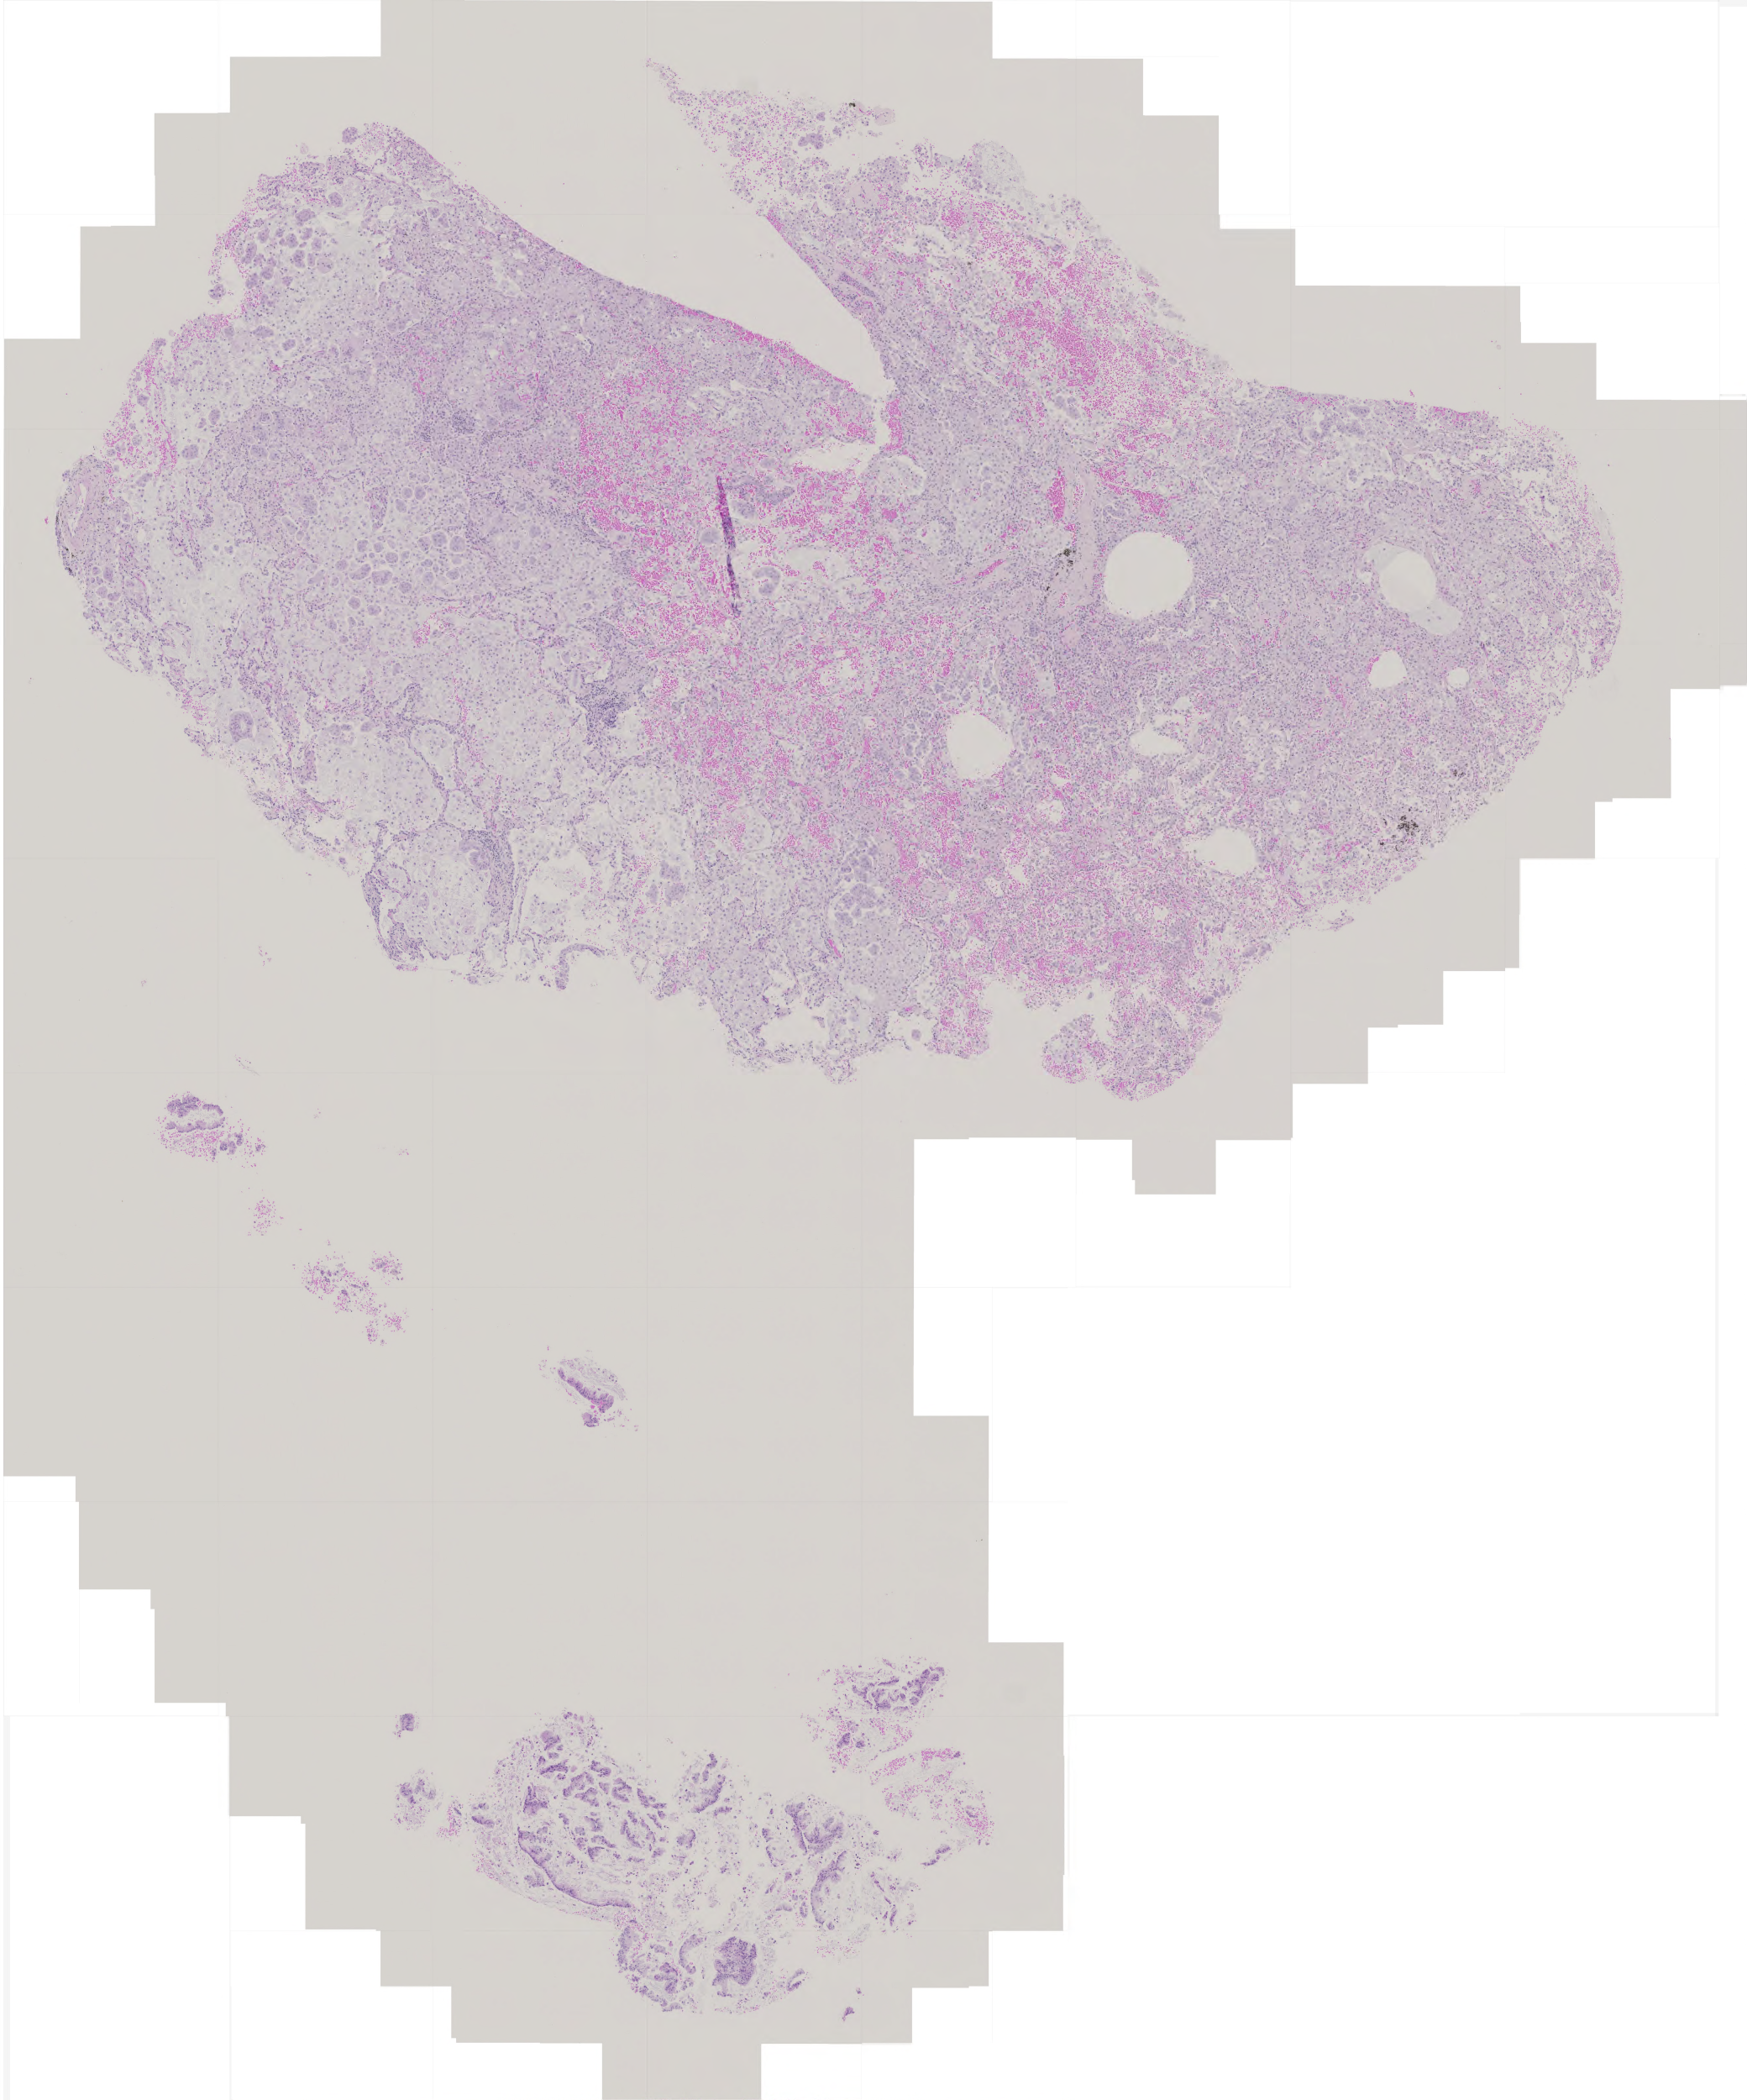
Whole-slide histology image, H&E-stained — low-resolution overview of the scanned area, about 4.2 x 5.0 mm; FFPE section; lung, primary tumour sample. Female, age 69 years at initial diagnosis.
AJCC pathologic stage: IB. Histologic diagnosis: Adenocarcinoma with mixed subtypes (upper lobe, lung).